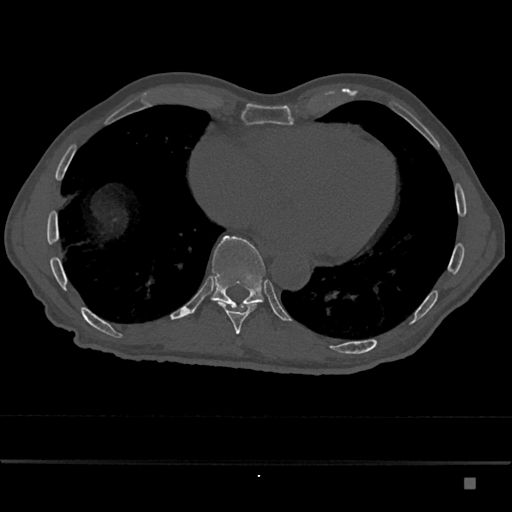
CT including the spine, one axial slice; slice 775 of 797 in the series (ordered by position); 120 kVp; bone window (W 1800 / L 400 HU); 0.5 mm slice thickness; 512 × 512 image matrix, field of view 390 × 390 mm. Male patient, age 72 years. From the clinical record (not read from this slice): primary cancer: prostate.
Structures marked on this image (semi-automatically segmented with operator editing):
- T10 vertebra: bounding box <210,236,266,310> (left, top, right, bottom; pixels)
- T9 vertebra: <219,303,256,335>